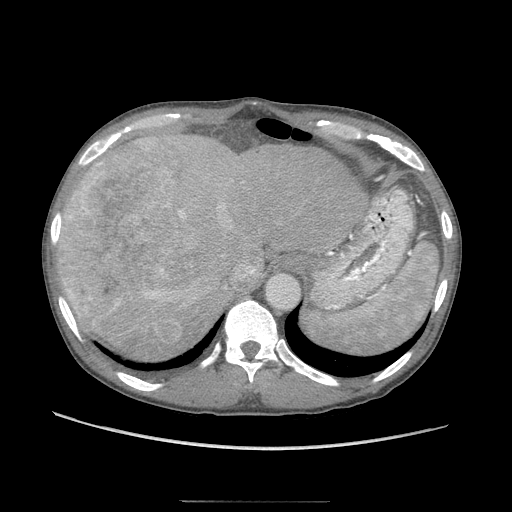
Contrast-enhanced abdominal CT (liver protocol), one axial slice; position 74 of 103 along the scan axis; reconstruction kernel STANDARD; soft-tissue window (W 400 / L 40 HU); 512 × 512 image matrix, field of view 380 × 380 mm. Case-level facts recorded for this patient, not image findings: diagnosis: hepatocellular carcinoma (patient treated with transarterial chemoembolisation; whether this scan precedes or follows treatment is not stated here); TNM stage (as recorded): Stage-IIIA; Child-Pugh class: A; tumour nodularity: multinodular; tumour size: 16 cm.
Outlined on this slice (semi-automatic segmentation, software-assisted and operator-edited):
- liver parenchyma outside the tumour (the mass and vessels are separate outlines, so this box may not span the whole liver): bounding box (x1, y1, x2, y2) in pixels: (56, 140, 364, 360)
- mass: (60, 153, 180, 347)
- liver vessels: (136, 153, 202, 326)